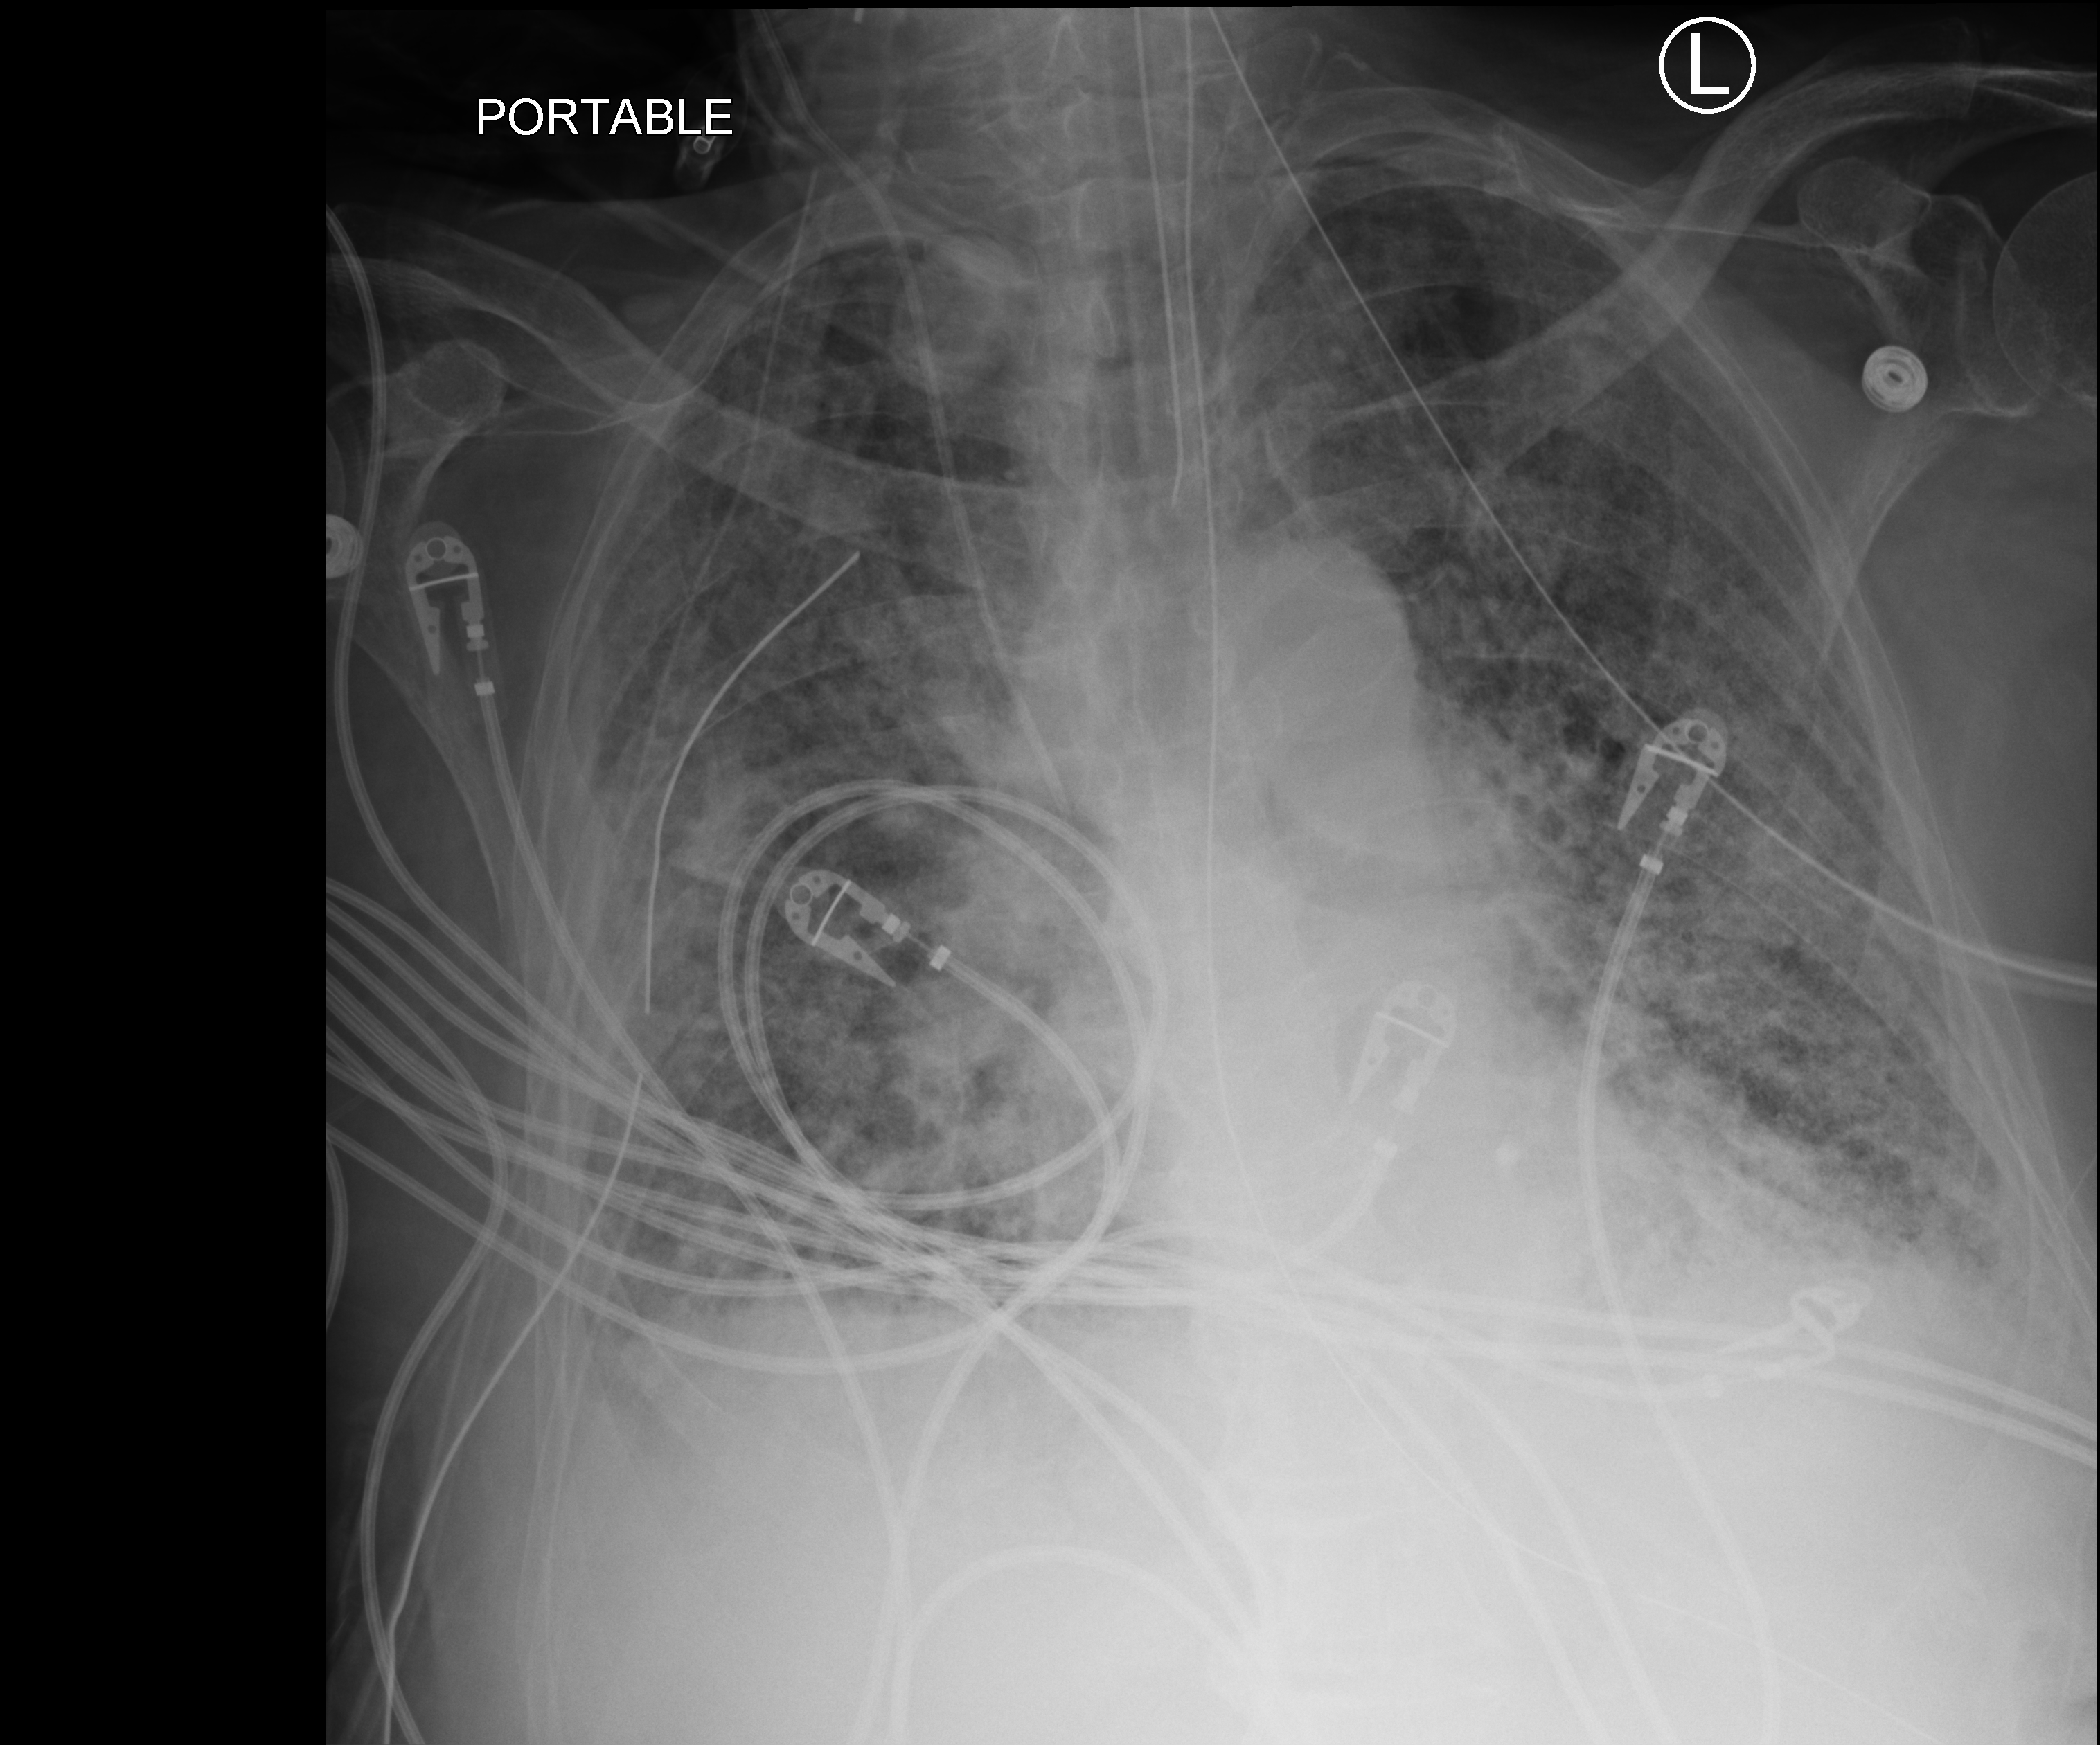
Bedside chest radiograph (computed radiography); anteroposterior (AP) projection. Patient hospitalised with COVID-19; male, aged 75–90 years.
Hospital-stay facts (about this admission, not read from this image; timing relative to this image not recorded):
- admitted to intensive care during this hospital stay: yes